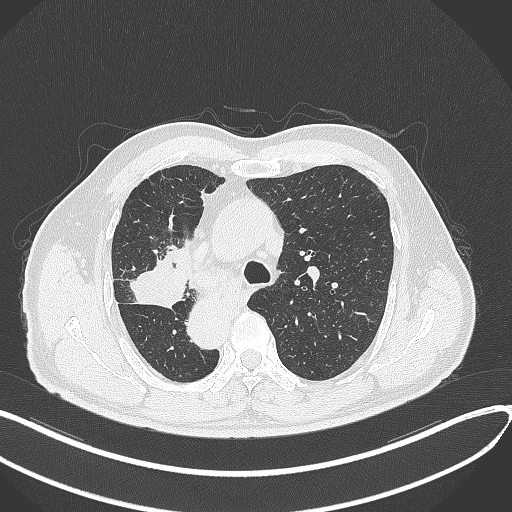
Chest CT, one axial slice; lung window (W 1500 / L -600 HU); 512 × 512 image matrix, field of view 400 × 400 mm. Male patient, age 67 years. From the clinical record (not read from this slice): clinical TNM (as recorded): T2a N0 M0.
Structures marked on this image (rectangle marked by the reading radiologist):
- lung tumour (recorded histology: squamous cell carcinoma): bounding box <128,258,192,311> (left, top, right, bottom; pixels)